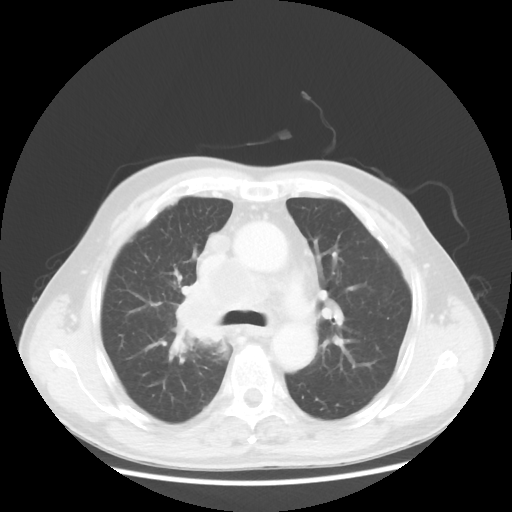
Chest CT, one axial slice; slice 80 of 124 in the series (ordered by position); 100 kVp; lung window (W 1500 / L -600 HU); 512 × 512 image matrix, field of view 382 × 382 mm. Patient: male, 64 years. Case-level facts recorded for this patient, not image findings: clinical TNM (as recorded): T3 N3 M0; histopathological grade: G3.
Structures marked on this image (bounding box drawn by a radiologist):
- lung tumour (recorded histology: small cell carcinoma): bounding box (x1, y1, x2, y2) in pixels: (168, 286, 239, 354)